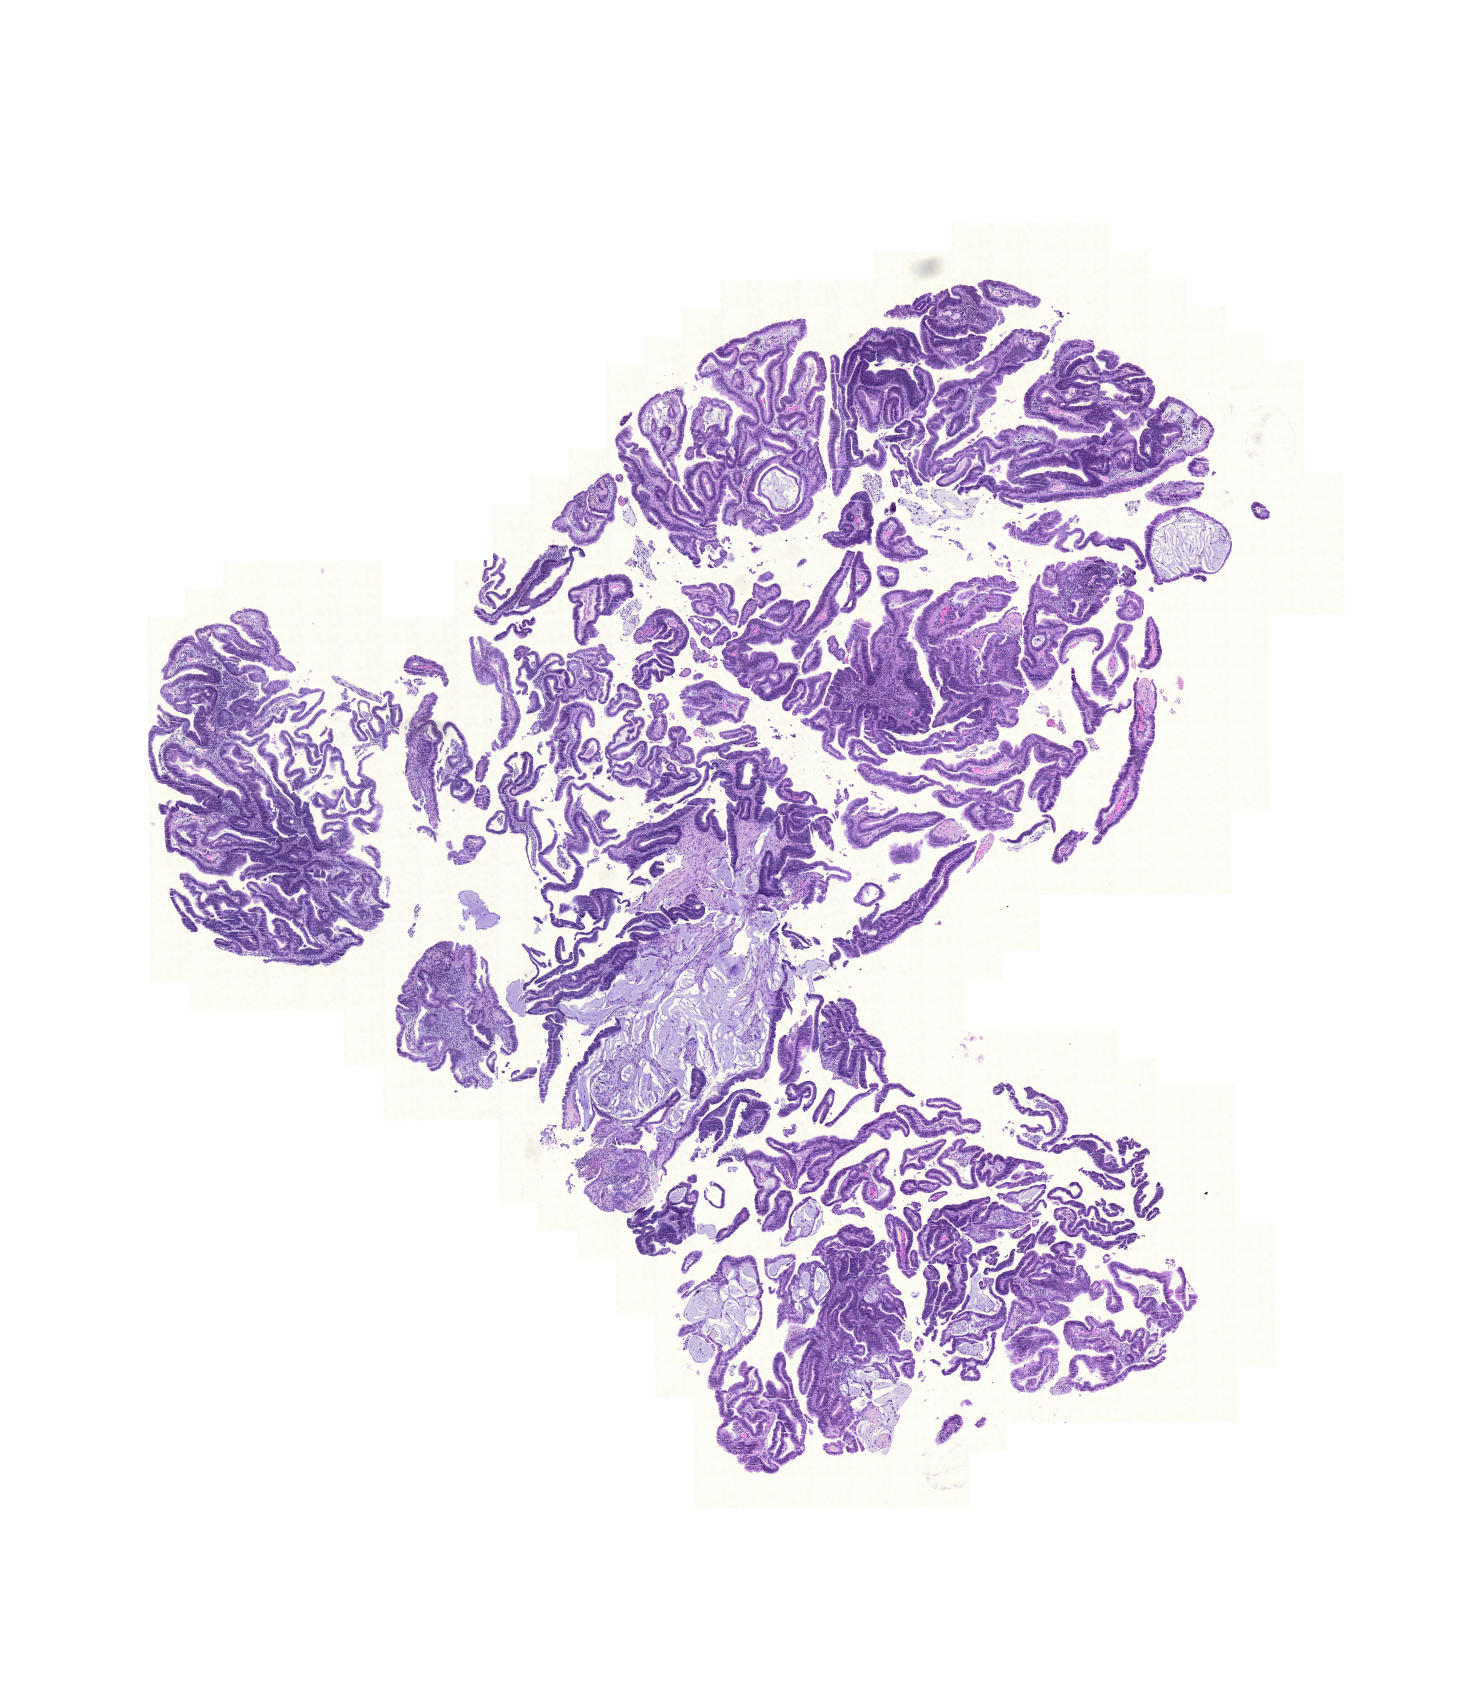
Whole-slide histology image, Hematoxylin and eosin (H&E) stained, shown as a low-resolution overview of the whole scanned area (about 11.0 x 12.7 mm, slide scanned at 20x). FFPE section. Sample: primary tumour, colon. Patient: male, age at initial diagnosis 75 years.
TNM: T4 N0 M0. Lymph nodes positive (case pathology): 0 of 21 examined. AJCC pathologic stage: IIB (6th edition). Diagnosis: Mucinous adenocarcinoma (cecum).